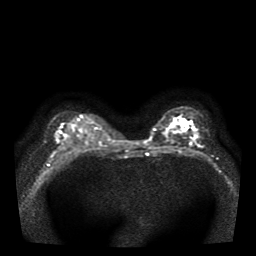
Breast MRI, one axial slice. Diffusion-weighted series; image 2 of 4 stored at this slice position (different b-values; order by instance number). 1.5 T. 5 mm slice thickness. 256 × 256 image matrix, field of view 330 × 330 mm. Female patient.
Structures marked on this image (manually delineated by an expert):
- tumour on diffusion-weighted imaging: box from (x=168, y=125) to (x=182, y=134) px